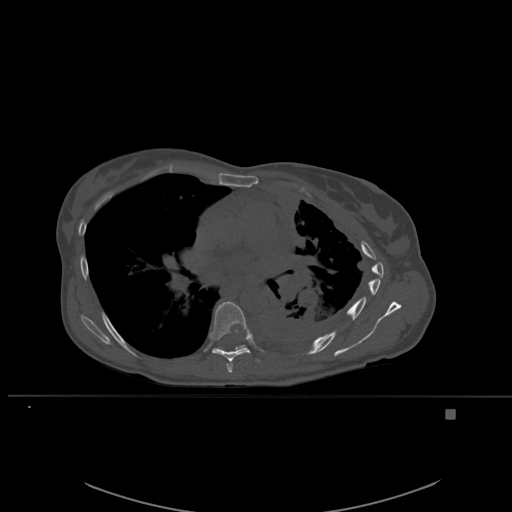
CT including the spine, one axial slice; slice 365 of 537 in the series (ordered by position); bone window (W 1800 / L 400 HU); 1.5 mm slice thickness; 512 × 512 image matrix, field of view 440 × 440 mm. Patient: female, 45 years. From the clinical record (not read from this slice): primary cancer: lung.
Annotated regions visible in this slice (semi-automatic segmentation, software-assisted and operator-edited):
- T6 vertebra: box from (x=226, y=360) to (x=233, y=373) px
- T7 vertebra: (x=210, y=301)–(x=260, y=362)
- T8 vertebra: (x=221, y=345)–(x=246, y=351)